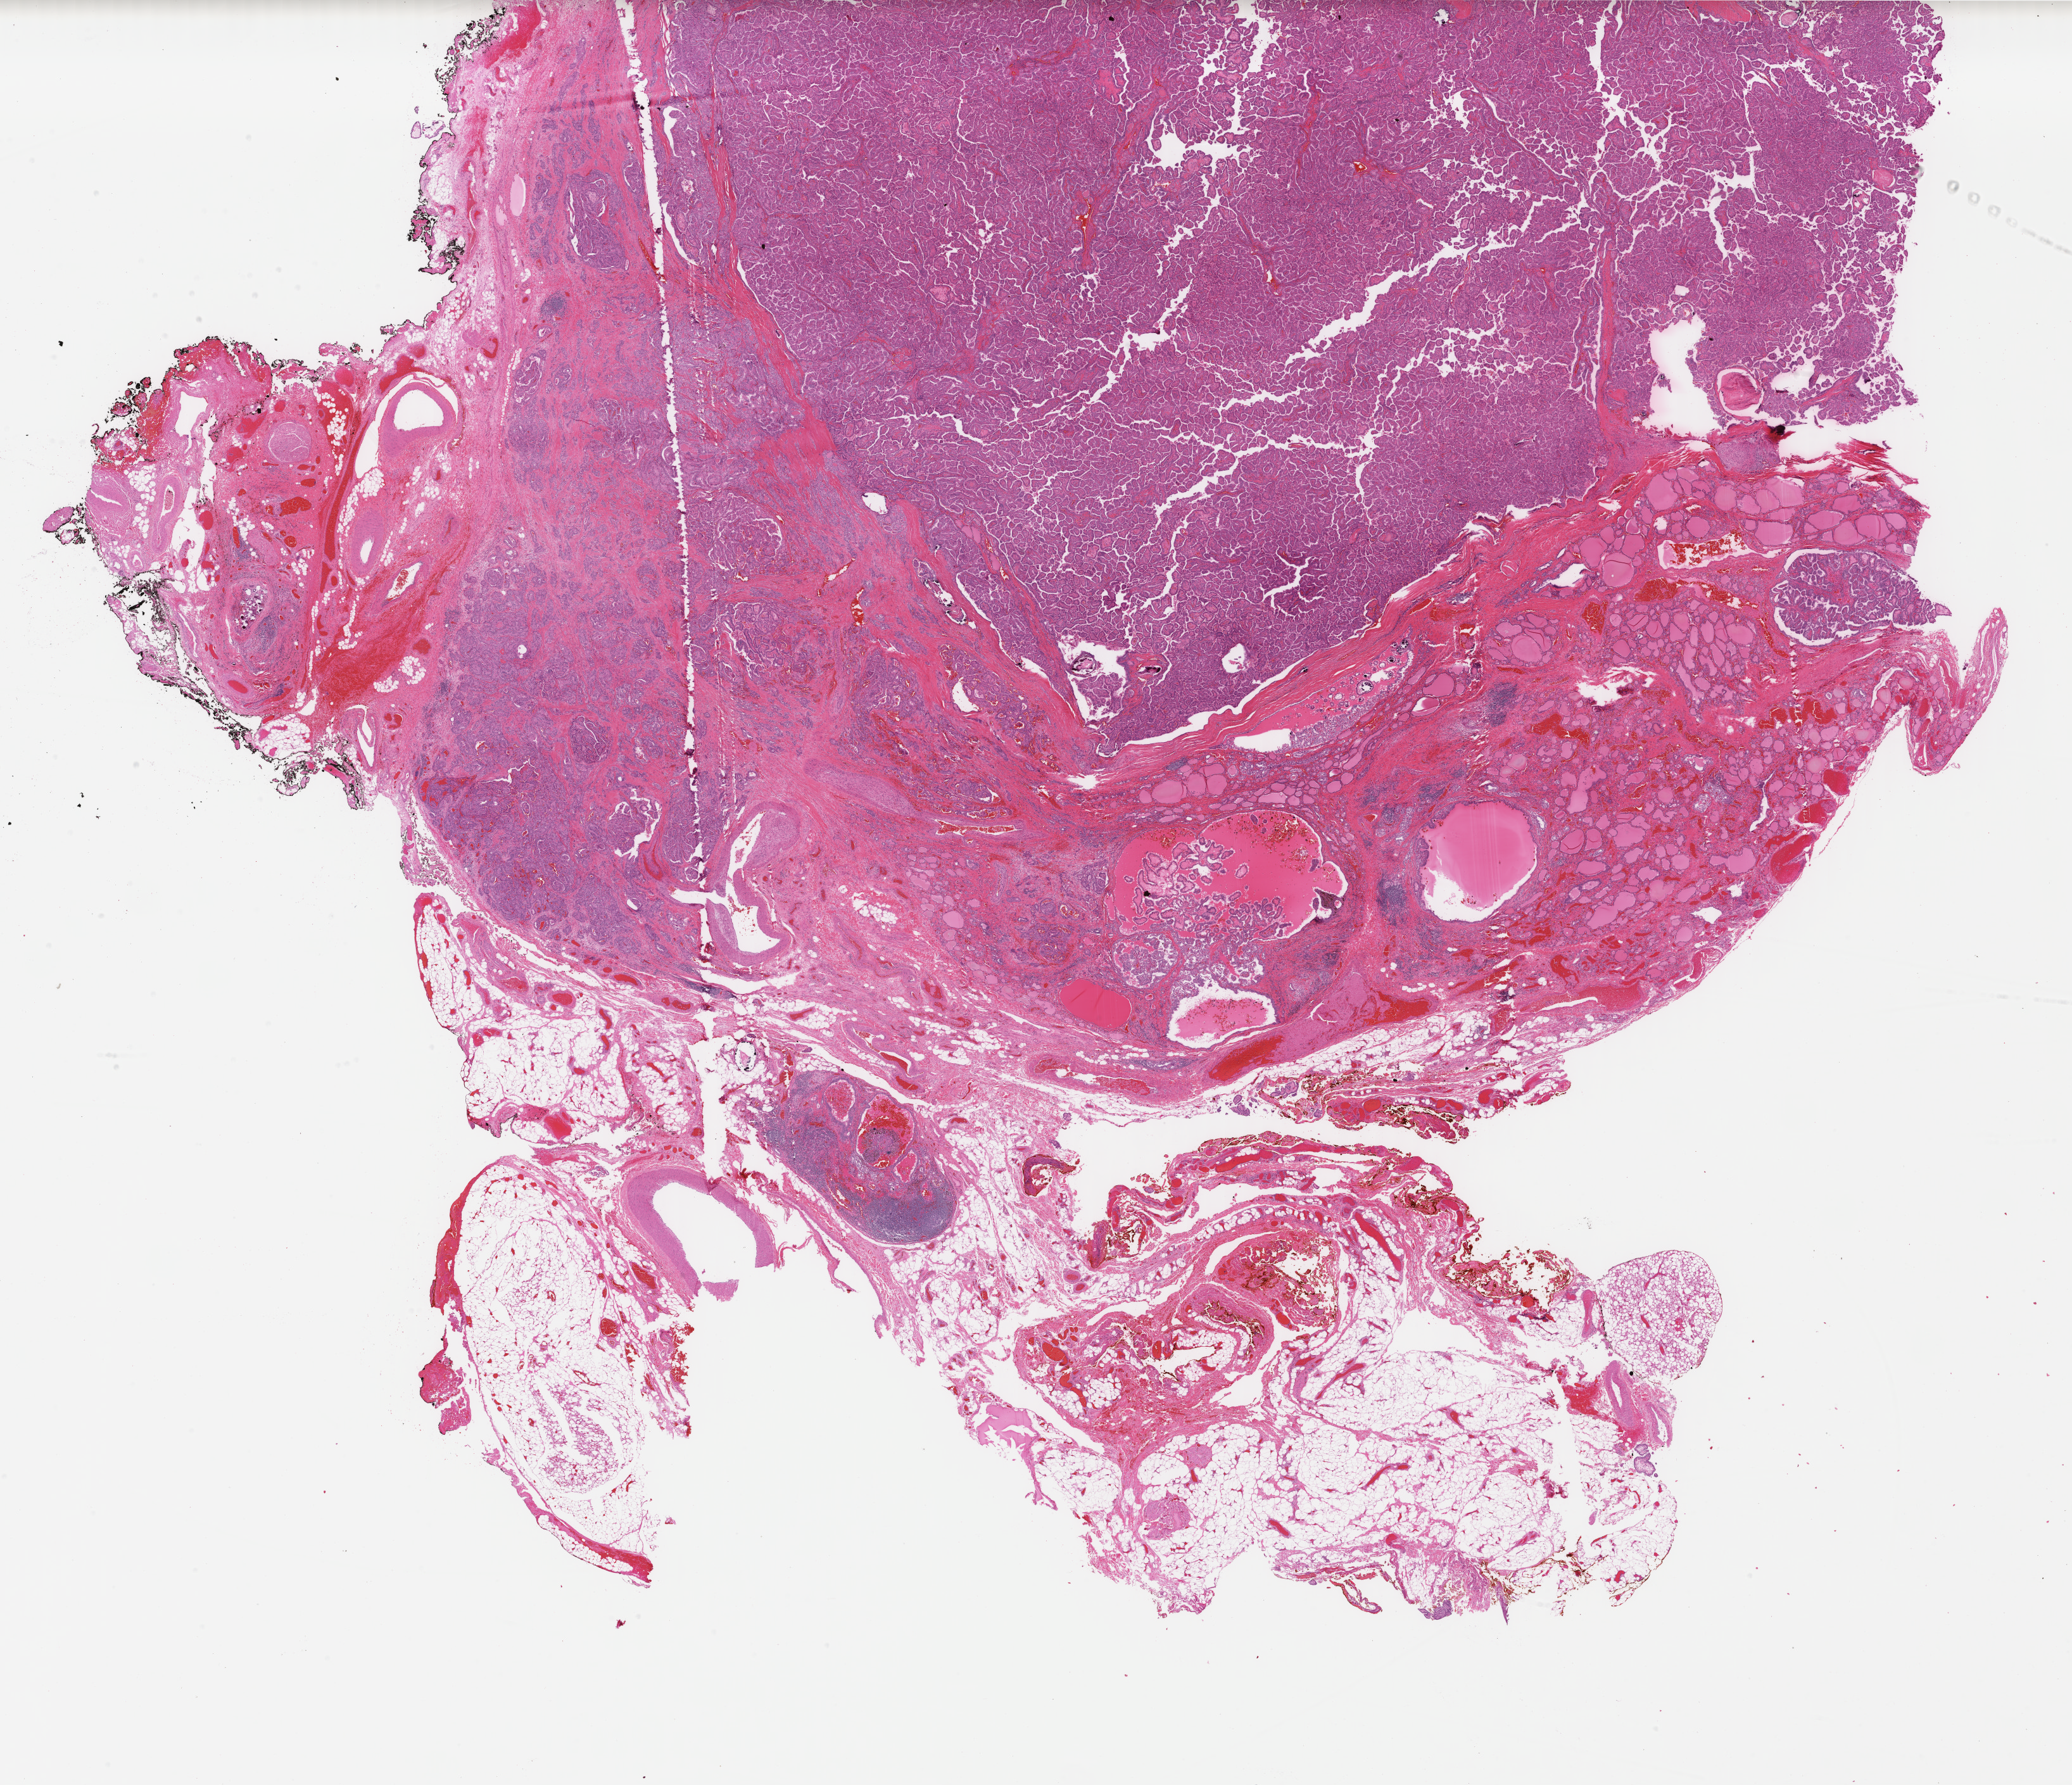
Whole-slide histology image, H&E, a low-resolution overview of the entire scanned area, about 26.0 x 22.4 mm. Formalin-fixed paraffin-embedded (FFPE) diagnostic section. Thyroid, primary tumour sample. Male, age 24 years at initial diagnosis.
Diagnosis: Papillary adenocarcinoma, NOS (thyroid gland).